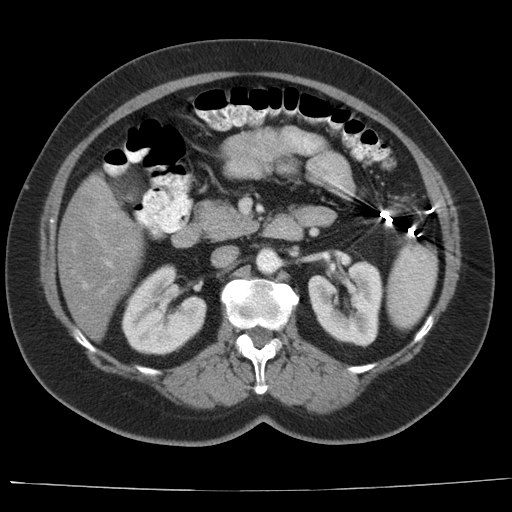
Contrast-enhanced abdominal CT, one axial slice; slice 11 of 44 in the series (ordered by position); reconstruction kernel AA-1; intravenous contrast given; soft-tissue window (W 400 / L 40 HU); 5 mm slice thickness; 512 × 512 image matrix. Female patient. Case-level facts recorded for this patient, not image findings: diagnosis: colorectal cancer liver metastases, imaged before liver resection.
Structures marked on this image (manually delineated by an expert):
- hepatic veins: box from (x=82, y=283) to (x=87, y=289) px
- liver: (x=60, y=176)–(x=143, y=339)
- portal vein (with intrahepatic branches): (x=101, y=261)–(x=114, y=293)
- liver metastasis: (x=82, y=191)–(x=100, y=209)
- liver metastasis: (x=97, y=206)–(x=136, y=246)